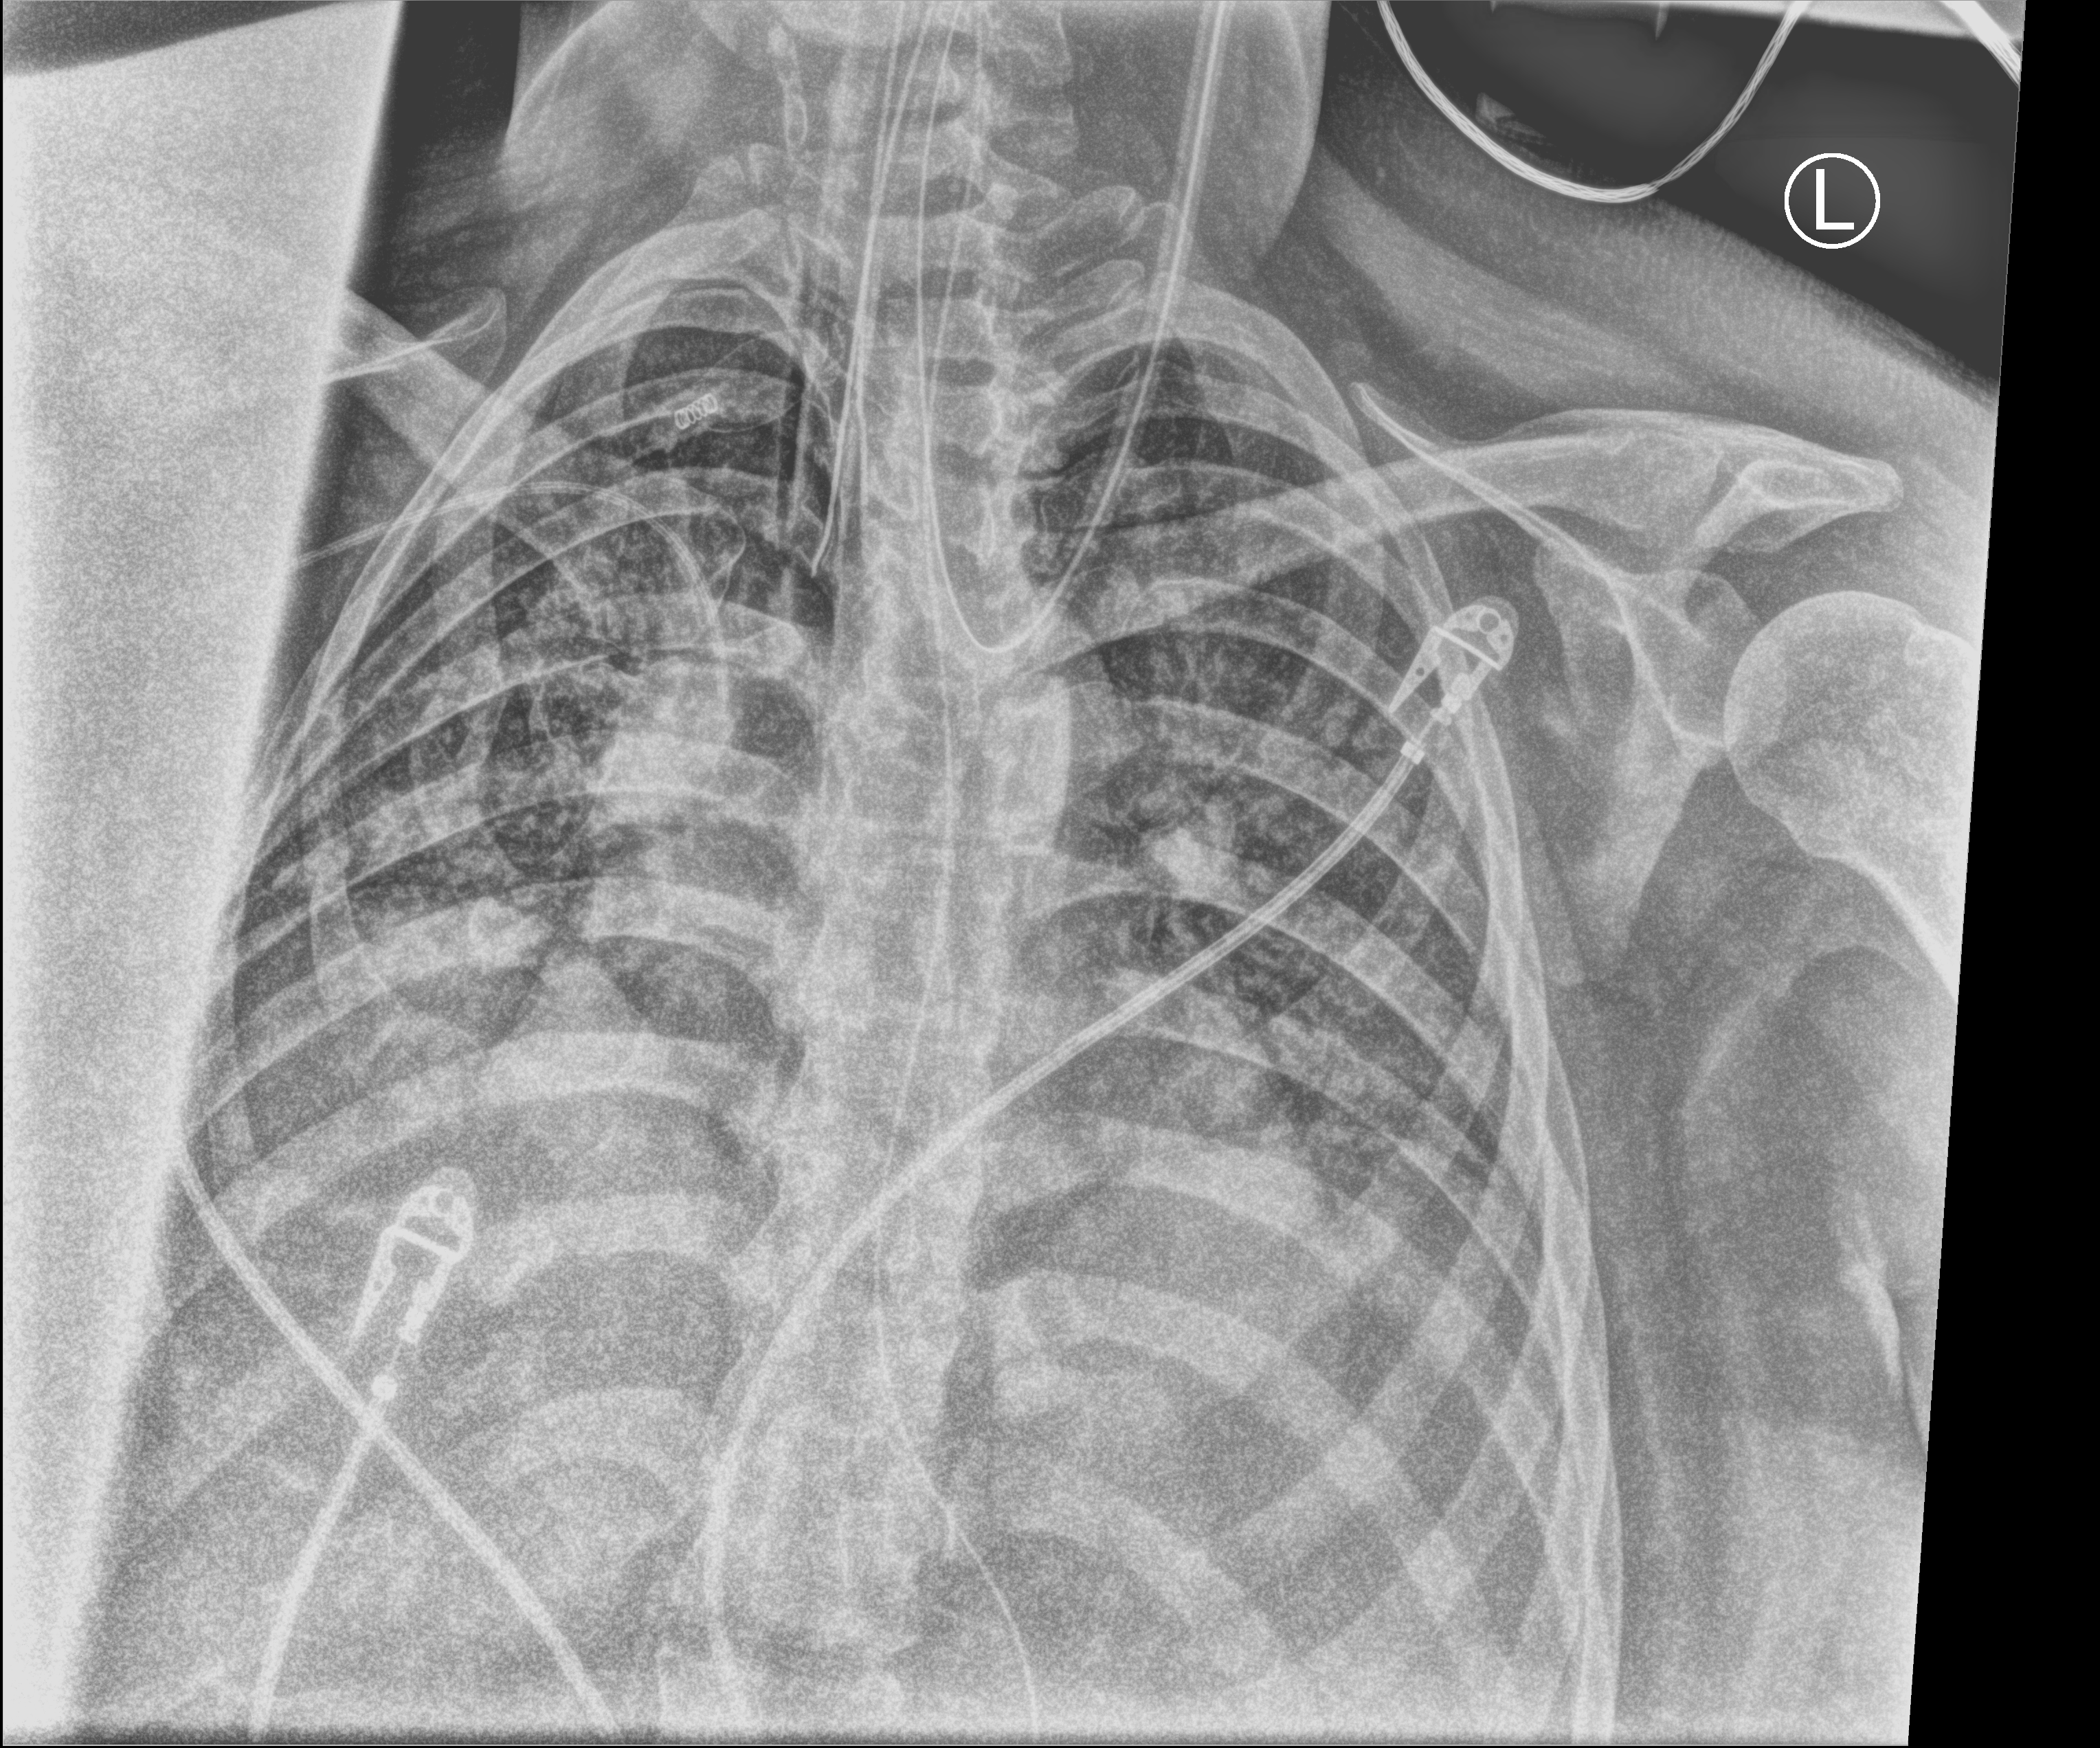
Bedside chest radiograph (computed radiography); anteroposterior (AP) projection. Female patient hospitalised with COVID-19, age 18–59 years.
From the hospital-stay record, not from the radiograph (when in the stay this image was taken is not recorded):
- chronic kidney disease (admission record): no